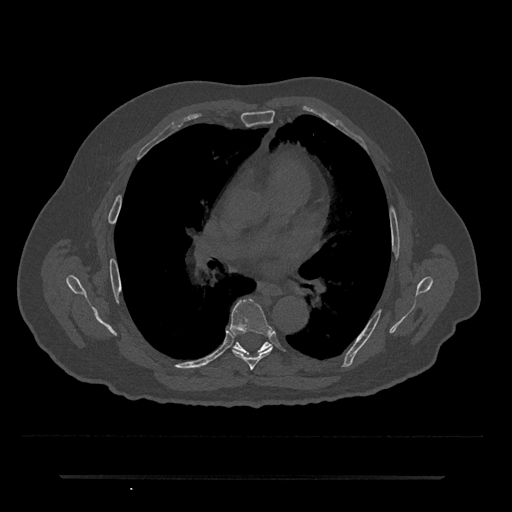
CT including the spine, one axial slice; reconstruction kernel Br40s/3; bone window (W 1800 / L 400 HU); 0.5 mm slice thickness; 512 × 512 image matrix, field of view 437 × 437 mm. Patient: male, 69 years. From the clinical record (not read from this slice): primary cancer: prostate.
Structures marked on this image (semi-automatically segmented with operator editing):
- T6 vertebra: bounding box (x1, y1, x2, y2) in pixels: (230, 299, 274, 370)
- T7 vertebra: (233, 342, 271, 354)